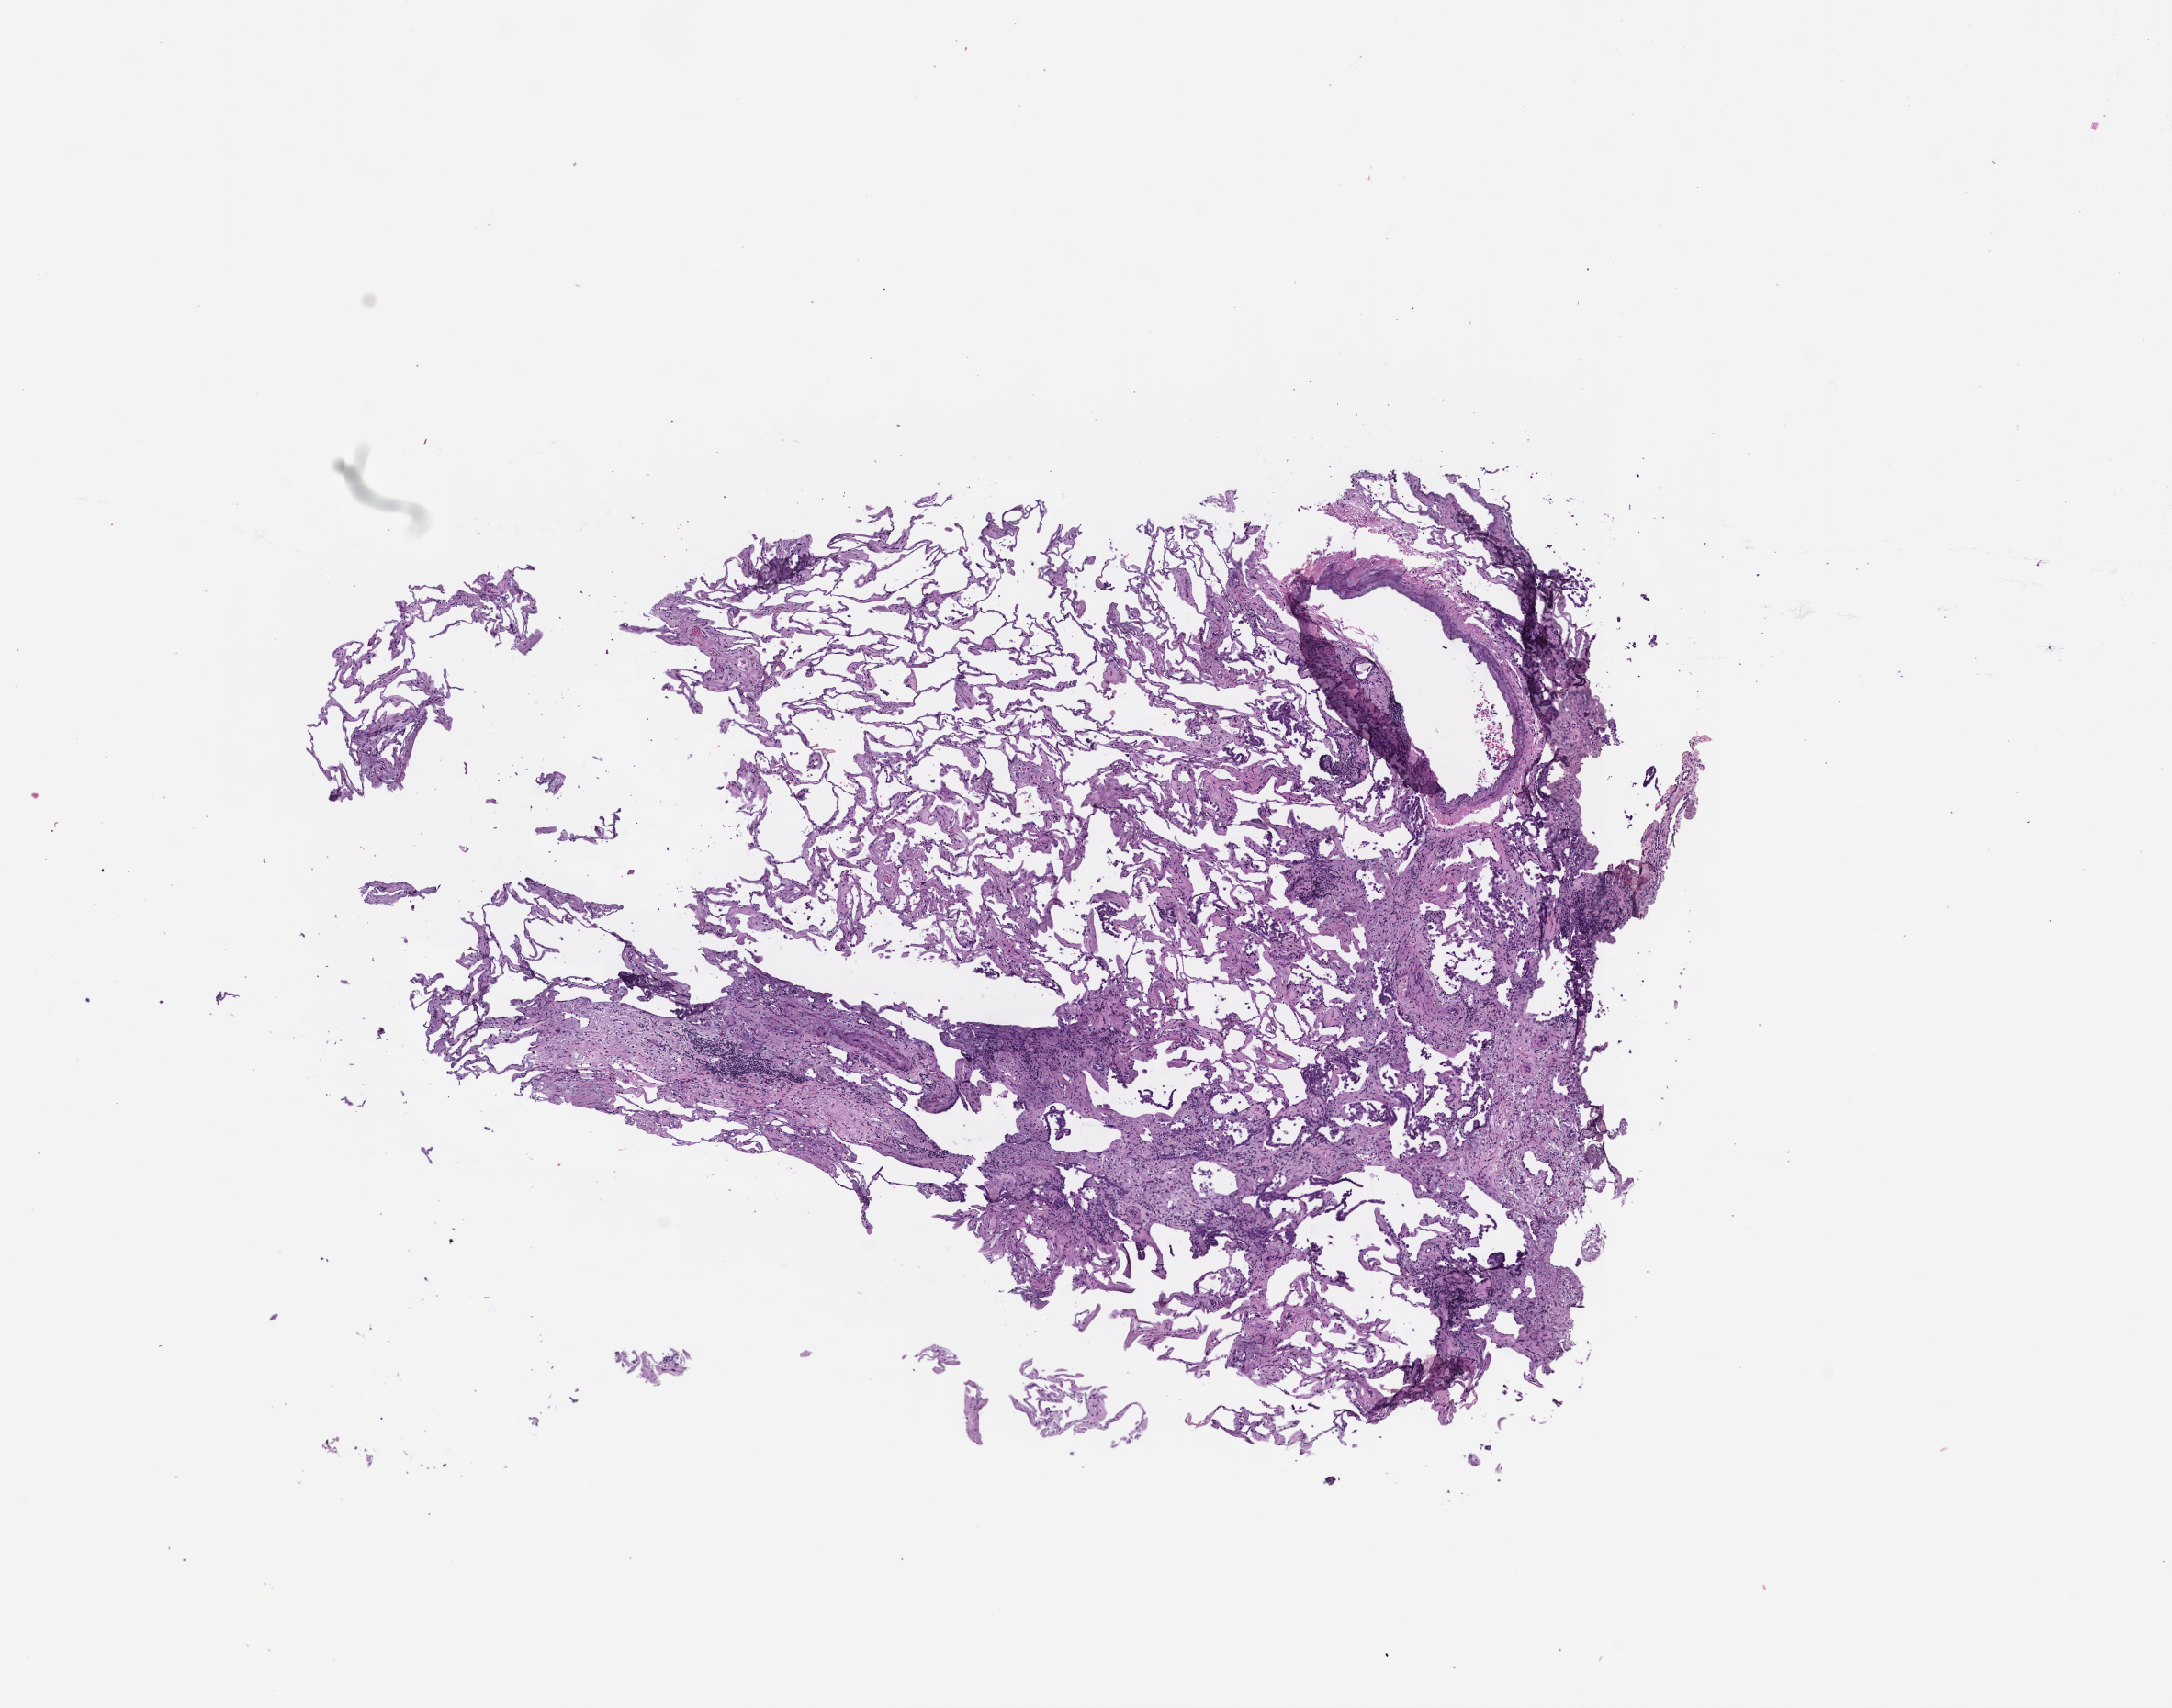
Digitized haematoxylin and eosin-stained section — a low-resolution overview of the entire scanned area, about 9.5 x 7.5 mm, FFPE section, tissue site: lung, specimen time point: collected on treatment. Patient: female.
This section: primary tumour tissue. Diagnosis: Non-Small Cell Lung Carcinoma.